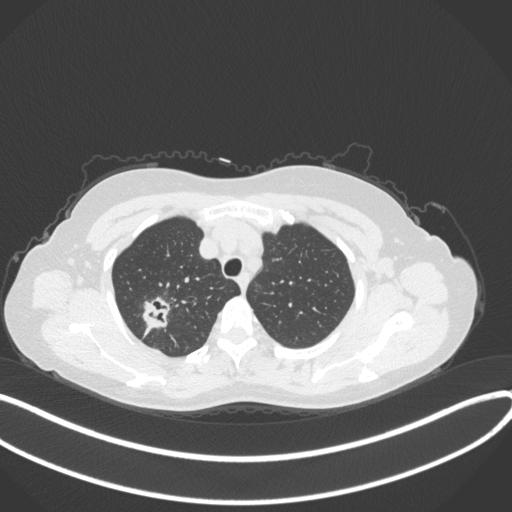
Chest CT, one axial slice. Slice 297 of 342 in the series (ordered by position). Reconstruction kernel B31f. 120 kVp. Lung window (W 1500 / L -600 HU). 1 mm slice thickness. 512 × 512 image matrix, field of view 400 × 400 mm. Patient: female, 50 years. Case-level facts recorded for this patient, not image findings: clinical TNM (as recorded): T1c N0 M0; histopathological grade: G2-3.
Structures marked on this image (rectangle marked by the reading radiologist):
- lung tumour (recorded histology: adenocarcinoma): bounding box <139,293,174,330> (left, top, right, bottom; pixels)